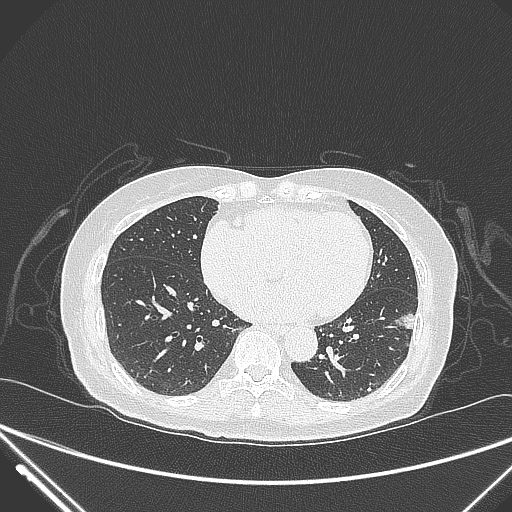
Chest CT, one axial slice; slice 115 of 310 in the series (ordered by position); 120 kVp; lung window (W 1500 / L -600 HU); 1 mm slice thickness; 512 × 512 image matrix, field of view 377 × 377 mm. Patient: female, 82 years. From the clinical record (not read from this slice): clinical TNM (as recorded): T1c N0 M0.
Annotated regions visible in this slice (rectangle marked by the reading radiologist):
- lung tumour (recorded histology: adenocarcinoma): bounding box (x1, y1, x2, y2) in pixels: (398, 309, 422, 339)